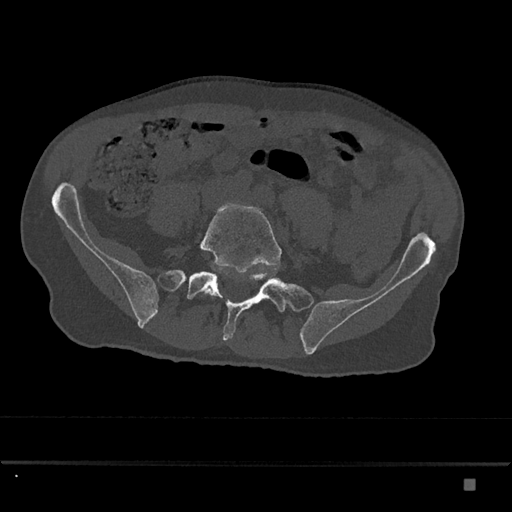
CT including the spine, one axial slice. Slice 255 of 797 in the series (ordered by position). Reconstruction kernel Br40s/3. 120 kVp. Bone window (W 1800 / L 400 HU). 0.5 mm slice thickness. 512 × 512 image matrix, field of view 390 × 390 mm. Male patient, age 72 years. From the clinical record (not read from this slice): primary cancer: prostate.
Annotated regions visible in this slice (semi-automatic segmentation, software-assisted and operator-edited):
- L5 vertebra: bounding box (x1, y1, x2, y2) in pixels: (199, 203, 282, 296)